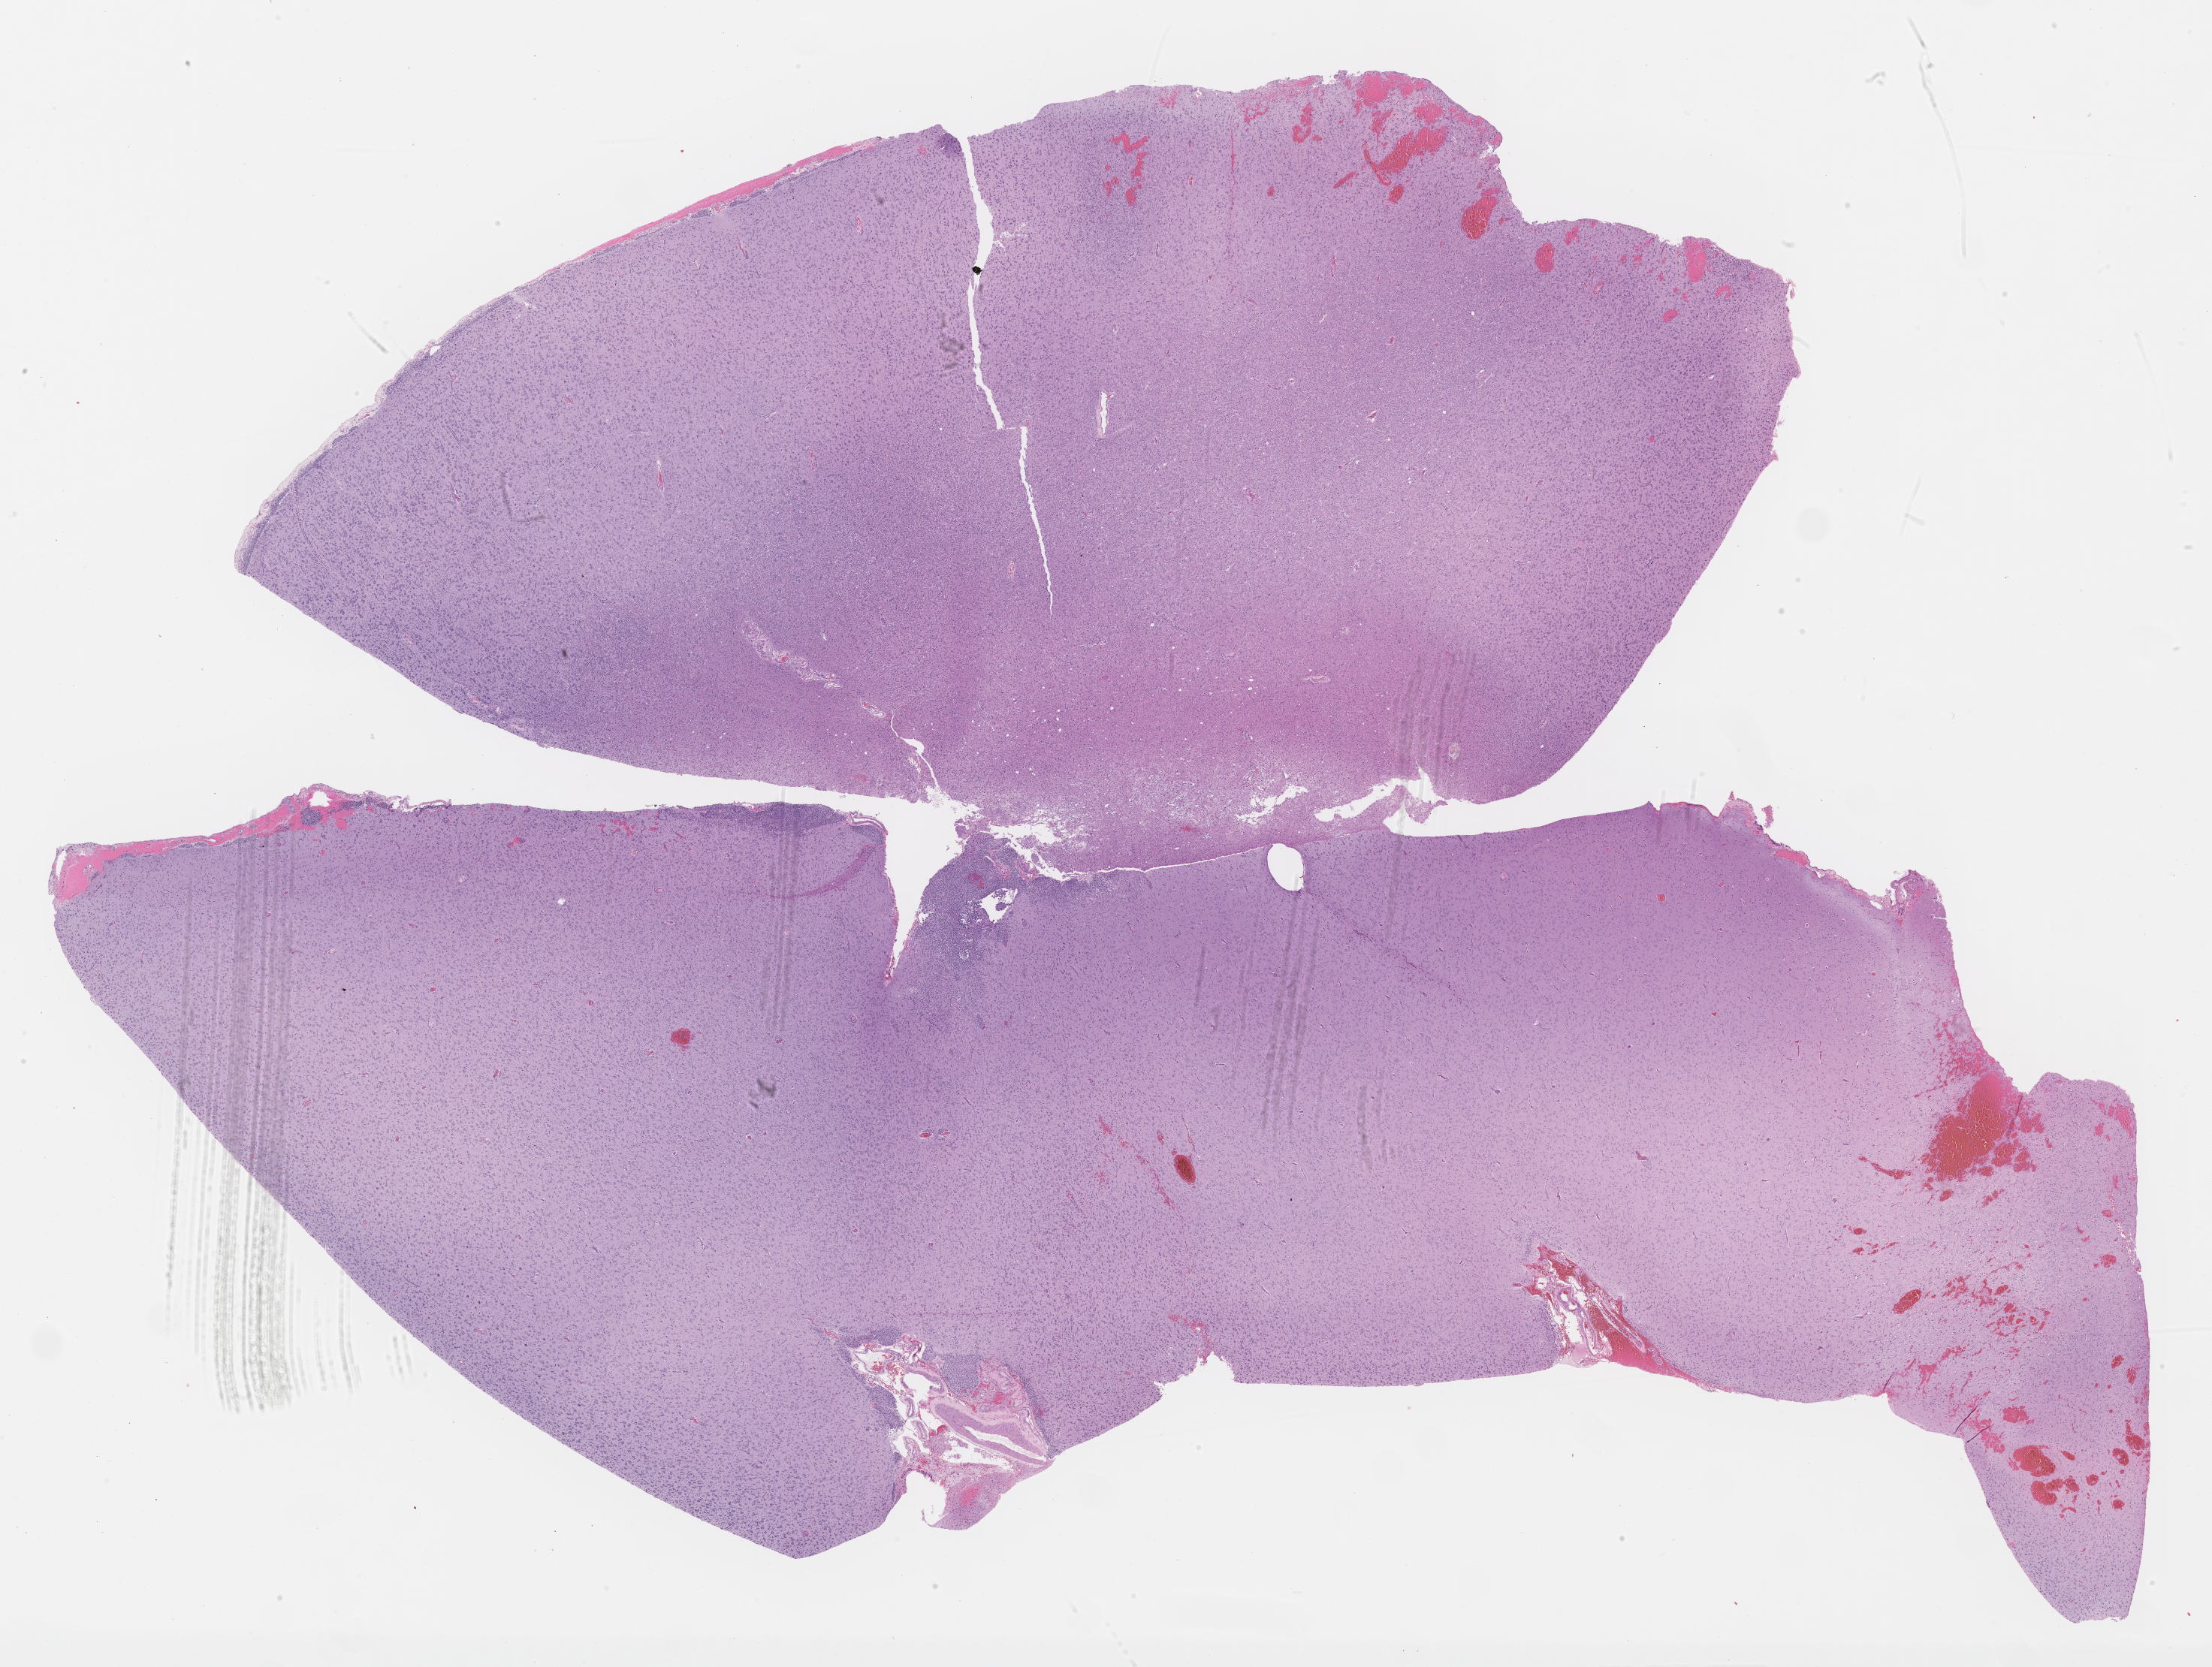
Whole-slide histology image, H&E-stained — whole scanned area (about 23.7 x 17.9 mm, from a 40x scan) shown as a low-resolution overview, formalin-fixed paraffin-embedded (FFPE) diagnostic section, brain, primary tumour sample. Patient: female, age at initial diagnosis 53 years.
Pathologic diagnosis: Oligodendroglioma, NOS (cerebrum).